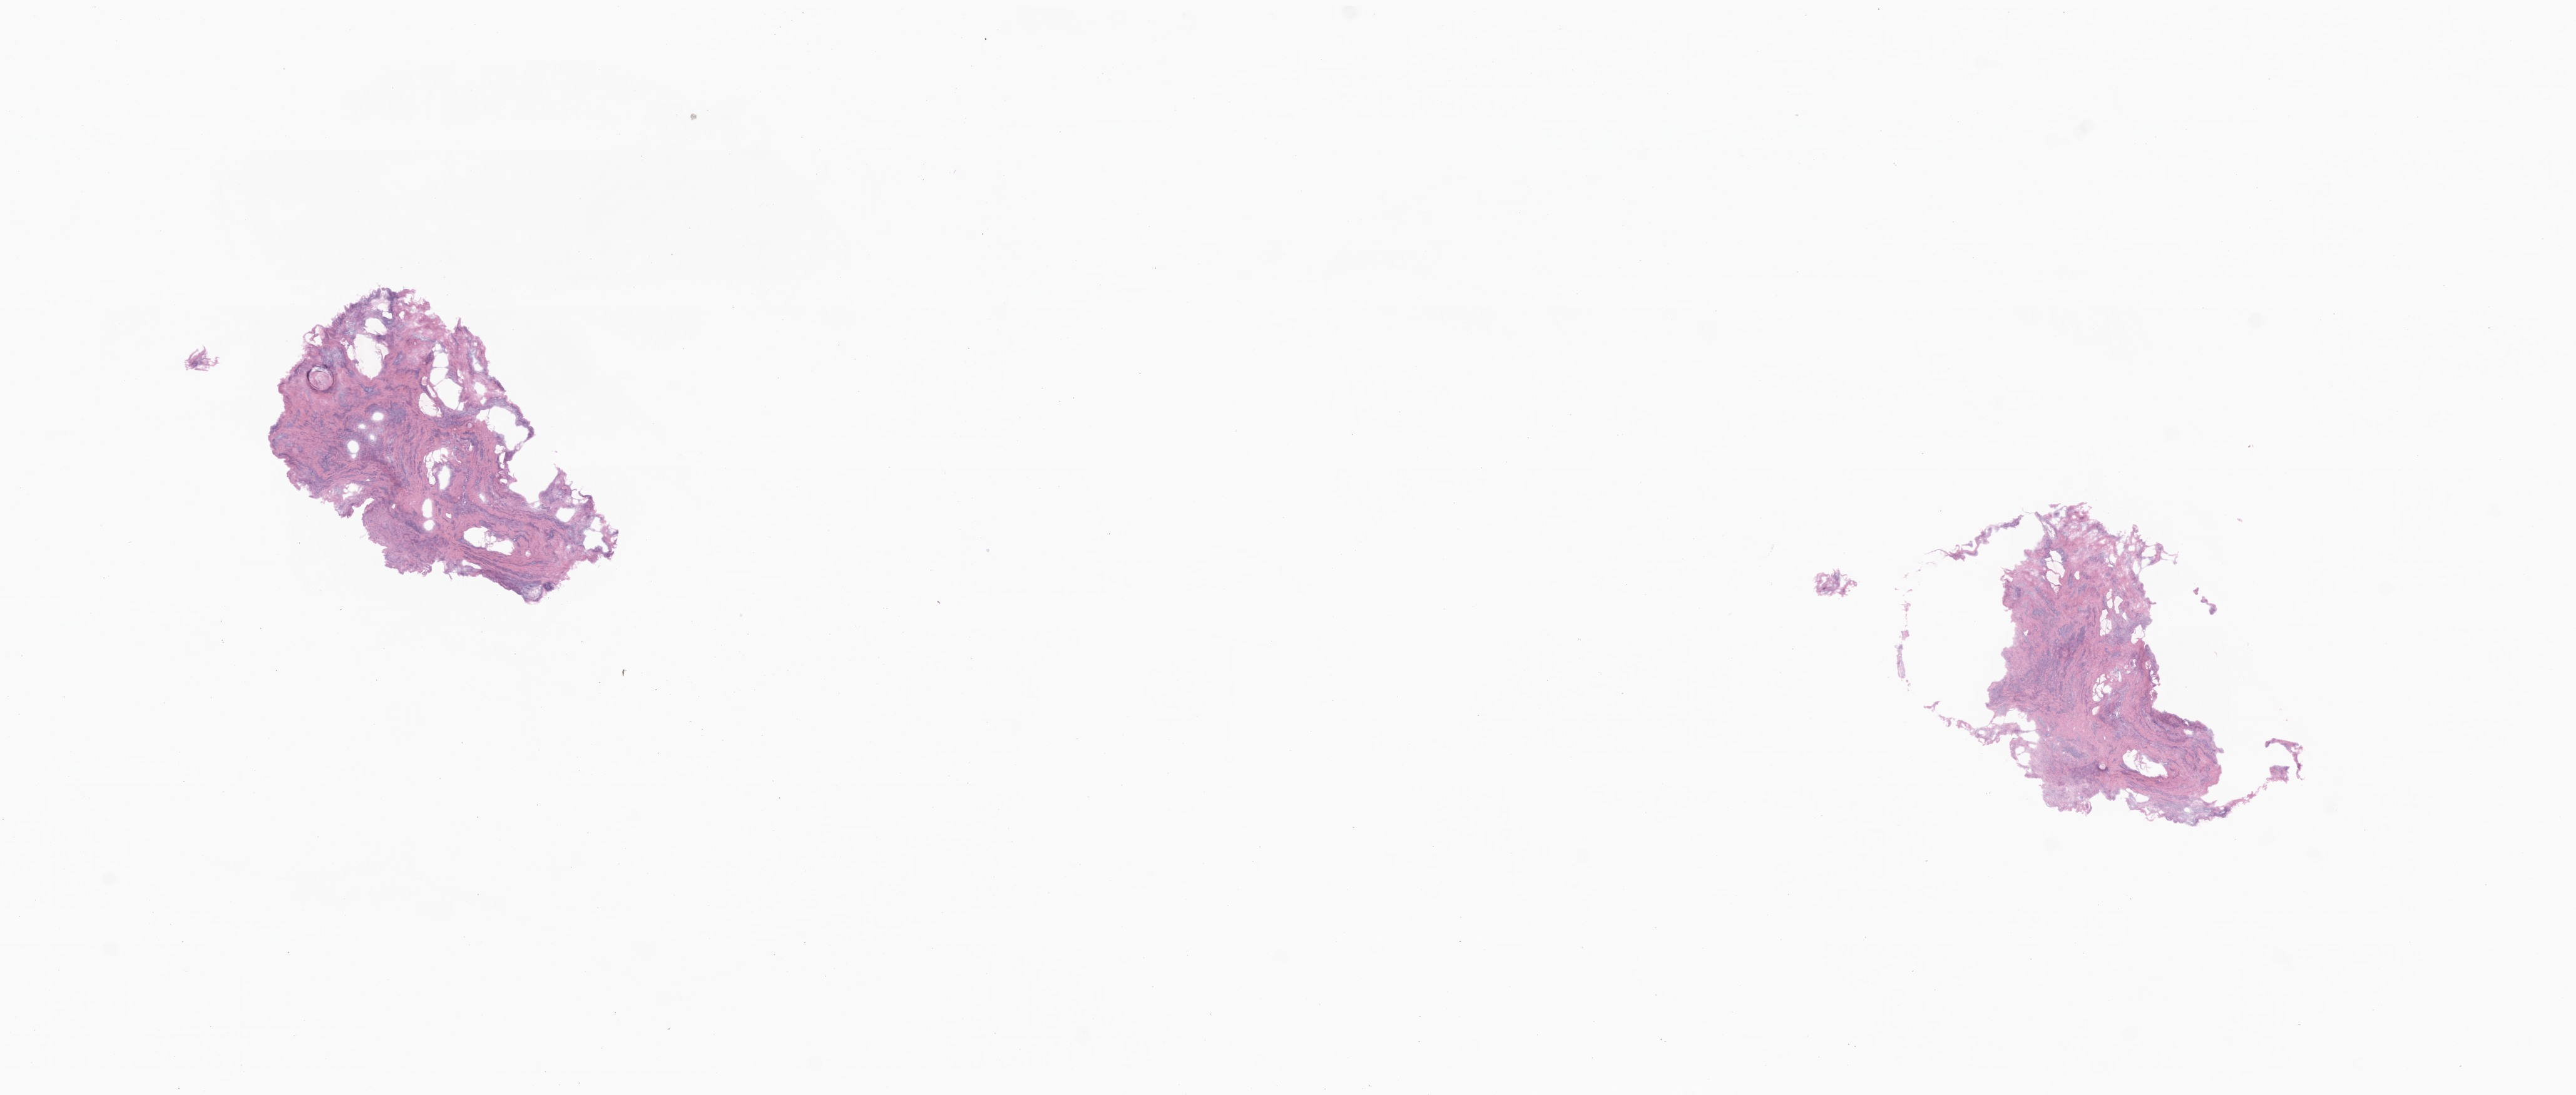
Whole-slide image, haematoxylin and eosin stain — low-resolution overview of the scanned area, about 17.3 x 7.4 mm; frozen section (tissue freezing medium); specimen: non-tumor (normal tissue) sample from a patient with serous borderline tumor, NOS; anatomic site: uterine adnexa. Patient sex: female. Composition of this section per pathologist review: tumor cells 0%, tumor nuclei 0%, stromal cells 100%, necrosis 0%, normal cells 0%. Inflammatory infiltration, as recorded: lymphocyte infiltration 0%, monocyte infiltration 0%, neutrophil infiltration 0%.
This section: non-tumor tissue sample; the patient's diagnosis is given above.